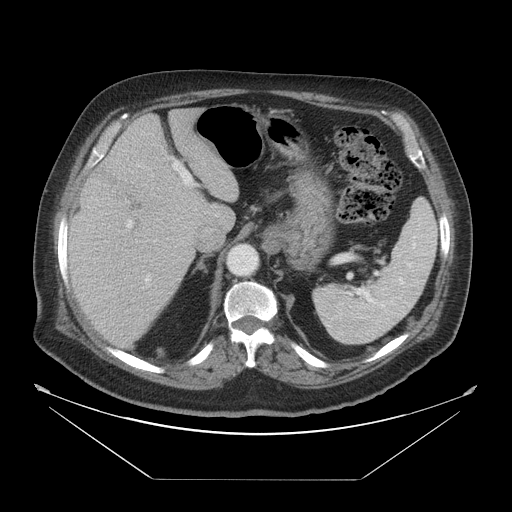
Contrast-enhanced abdominal CT, one axial slice. Position 35 of 45 along the scan axis. Reconstruction kernel STANDARD. 120 kVp. Intravenous contrast given. Soft-tissue window (W 400 / L 40 HU). 5 mm slice thickness. 512 × 512 image matrix, field of view 463 × 463 mm. Male patient, age 87 years. Case-level facts recorded for this patient, not image findings: diagnosis: colorectal cancer liver metastases, imaged before liver resection; multiple liver metastases: no; largest metastasis: 4.5 cm.
Annotated regions visible in this slice (expert manual segmentation):
- liver: box from (x=68, y=108) to (x=240, y=350) px
- planned liver remnant (the part of the liver to remain after resection): (x=115, y=108)–(x=240, y=200)
- portal vein (with intrahepatic branches): (x=127, y=156)–(x=198, y=289)
- liver metastasis: (x=131, y=215)–(x=143, y=237)
- liver metastasis: (x=93, y=162)–(x=147, y=207)